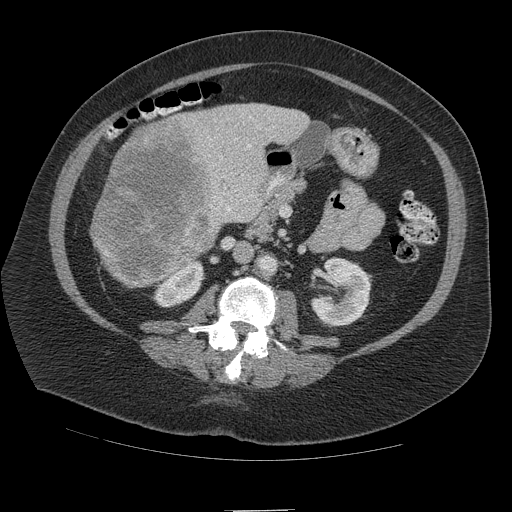
Contrast-enhanced abdominal CT (liver protocol), one axial slice; reconstruction kernel STANDARD; soft-tissue window (W 400 / L 40 HU); 2.5 mm slice thickness; 512 × 512 image matrix, field of view 420 × 420 mm. From the clinical record (not read from this slice): diagnosis: hepatocellular carcinoma (patient treated with transarterial chemoembolisation; whether this scan precedes or follows treatment is not stated here); TNM stage (as recorded): Stage-IVB; Child-Pugh class: A; tumour differentiation: poorly differentiated.
Structures marked on this image (semi-automatic segmentation, software-assisted and operator-edited):
- liver parenchyma outside the tumour (the mass and vessels are separate outlines, so this box may not span the whole liver): bounding box (x1, y1, x2, y2) in pixels: (100, 102, 310, 288)
- mass: (89, 116, 218, 288)
- liver vessels: (220, 144, 251, 212)